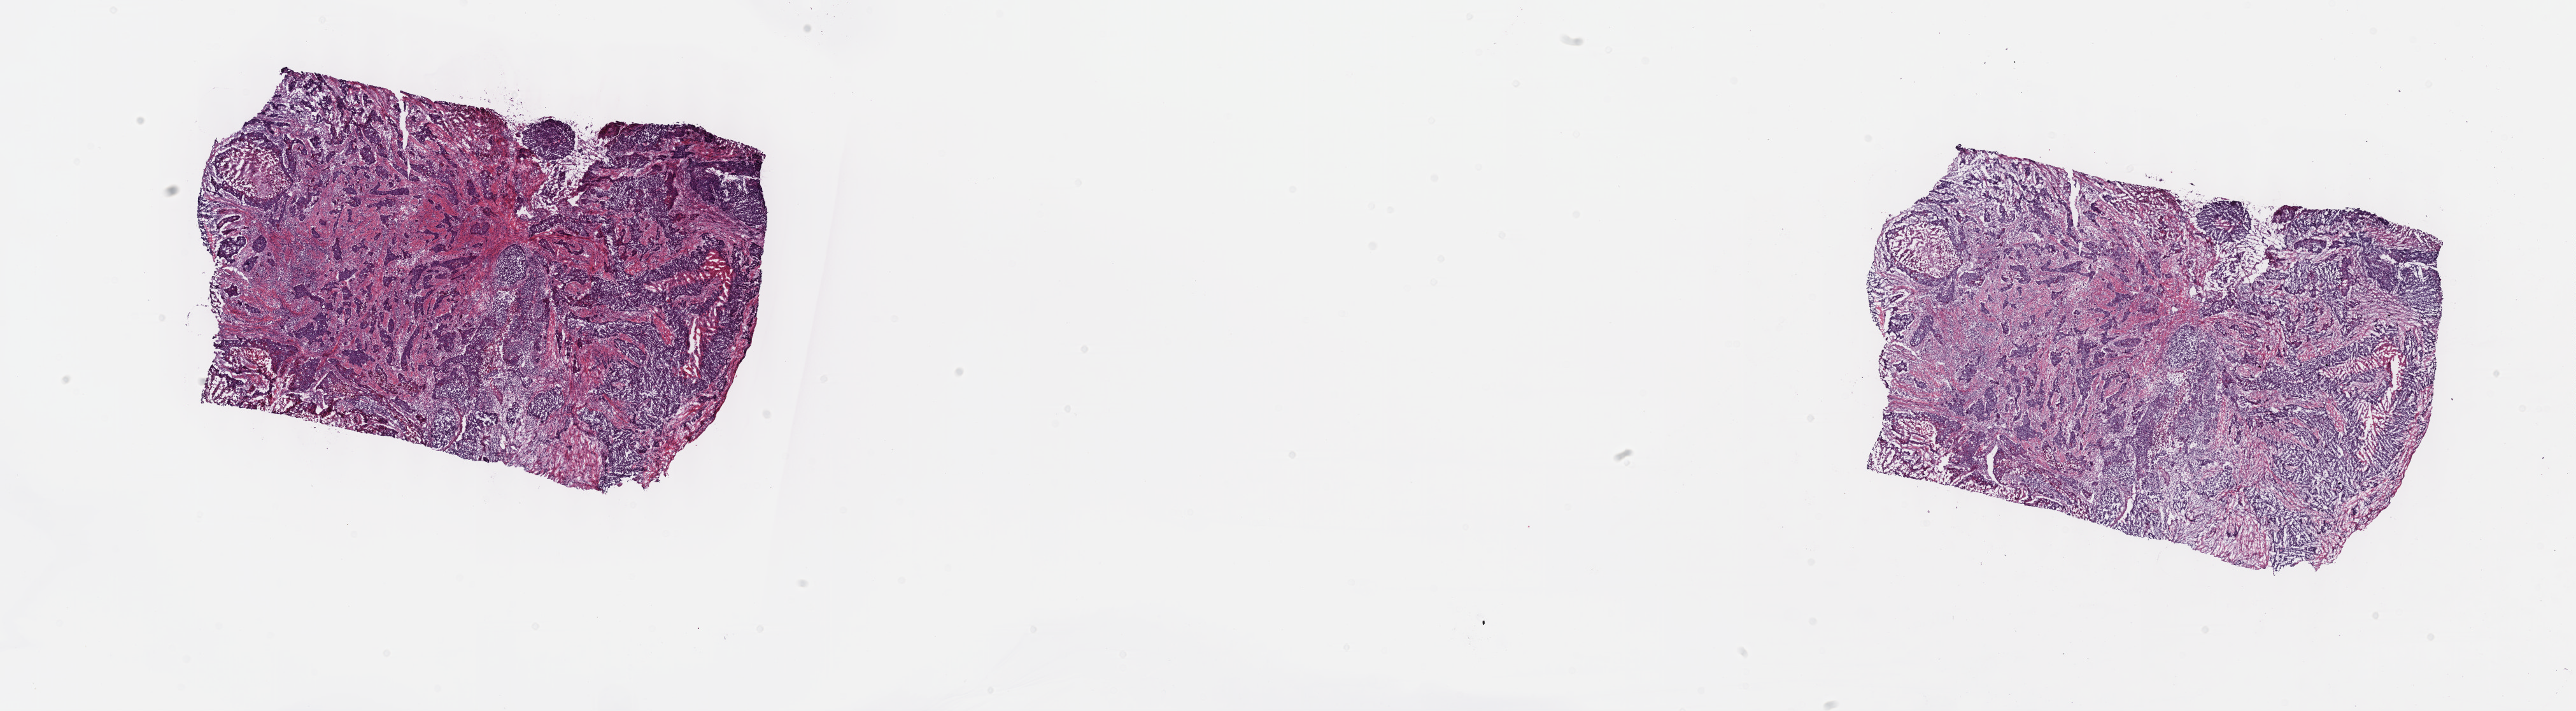
Hematoxylin and eosin (H&E) stained whole-slide image — low-resolution overview of the scanned area, about 32.7 x 9.0 mm; frozen section; sample: primary tumour, esophagus. Male patient; age at initial diagnosis 57 years. Histologic grade: G3 (poorly differentiated). Slide review estimates, as recorded: tumour cells 70%, tumour nuclei 70%, normal cells 0%, stromal cells 25%, necrosis 5%. Inflammatory infiltration, as recorded: lymphocyte infiltration 4%, monocyte infiltration 2%, neutrophil infiltration 3%.
Pathologic diagnosis: Squamous cell carcinoma, NOS. AJCC pathologic stage: IIIA (7th edition). Lymph nodes positive (case pathology): 1 of 9 examined.